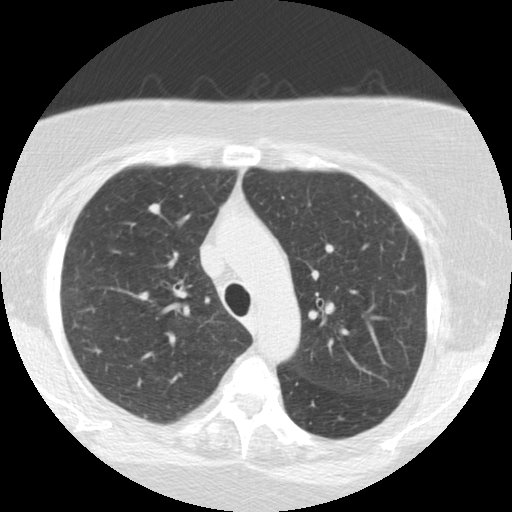
Low-dose screening chest CT, axial slice. Second screening round (one year after baseline). Lung window (W 1500 / L -600 HU). 2.5 mm slice thickness. Standard (soft-tissue) reconstruction kernel (STANDARD). Slice 170 of 225 in the series. 512 × 512 image matrix, field of view 320 × 320 mm. Female, age 64 years at enrolment.
- Expert reader's lesion annotation, box from (x=129, y=194) to (x=170, y=231) px.
- Screening reader's record for this exam (one nodule recorded; not confirmed to be the boxed lesion): non-calcified nodule or mass ≥4 mm, right upper lobe, 8 × 7 mm, smooth margins, soft tissue attenuation, pre-existing on the prior screen: no.
- Official screen result: positive, other.
- Later outcome: lung cancer diagnosed 85 days after this screen — large cell neuroendocrine carcinoma, right upper lobe, stage IA (AJCC 6th edition), 12 mm at pathology.